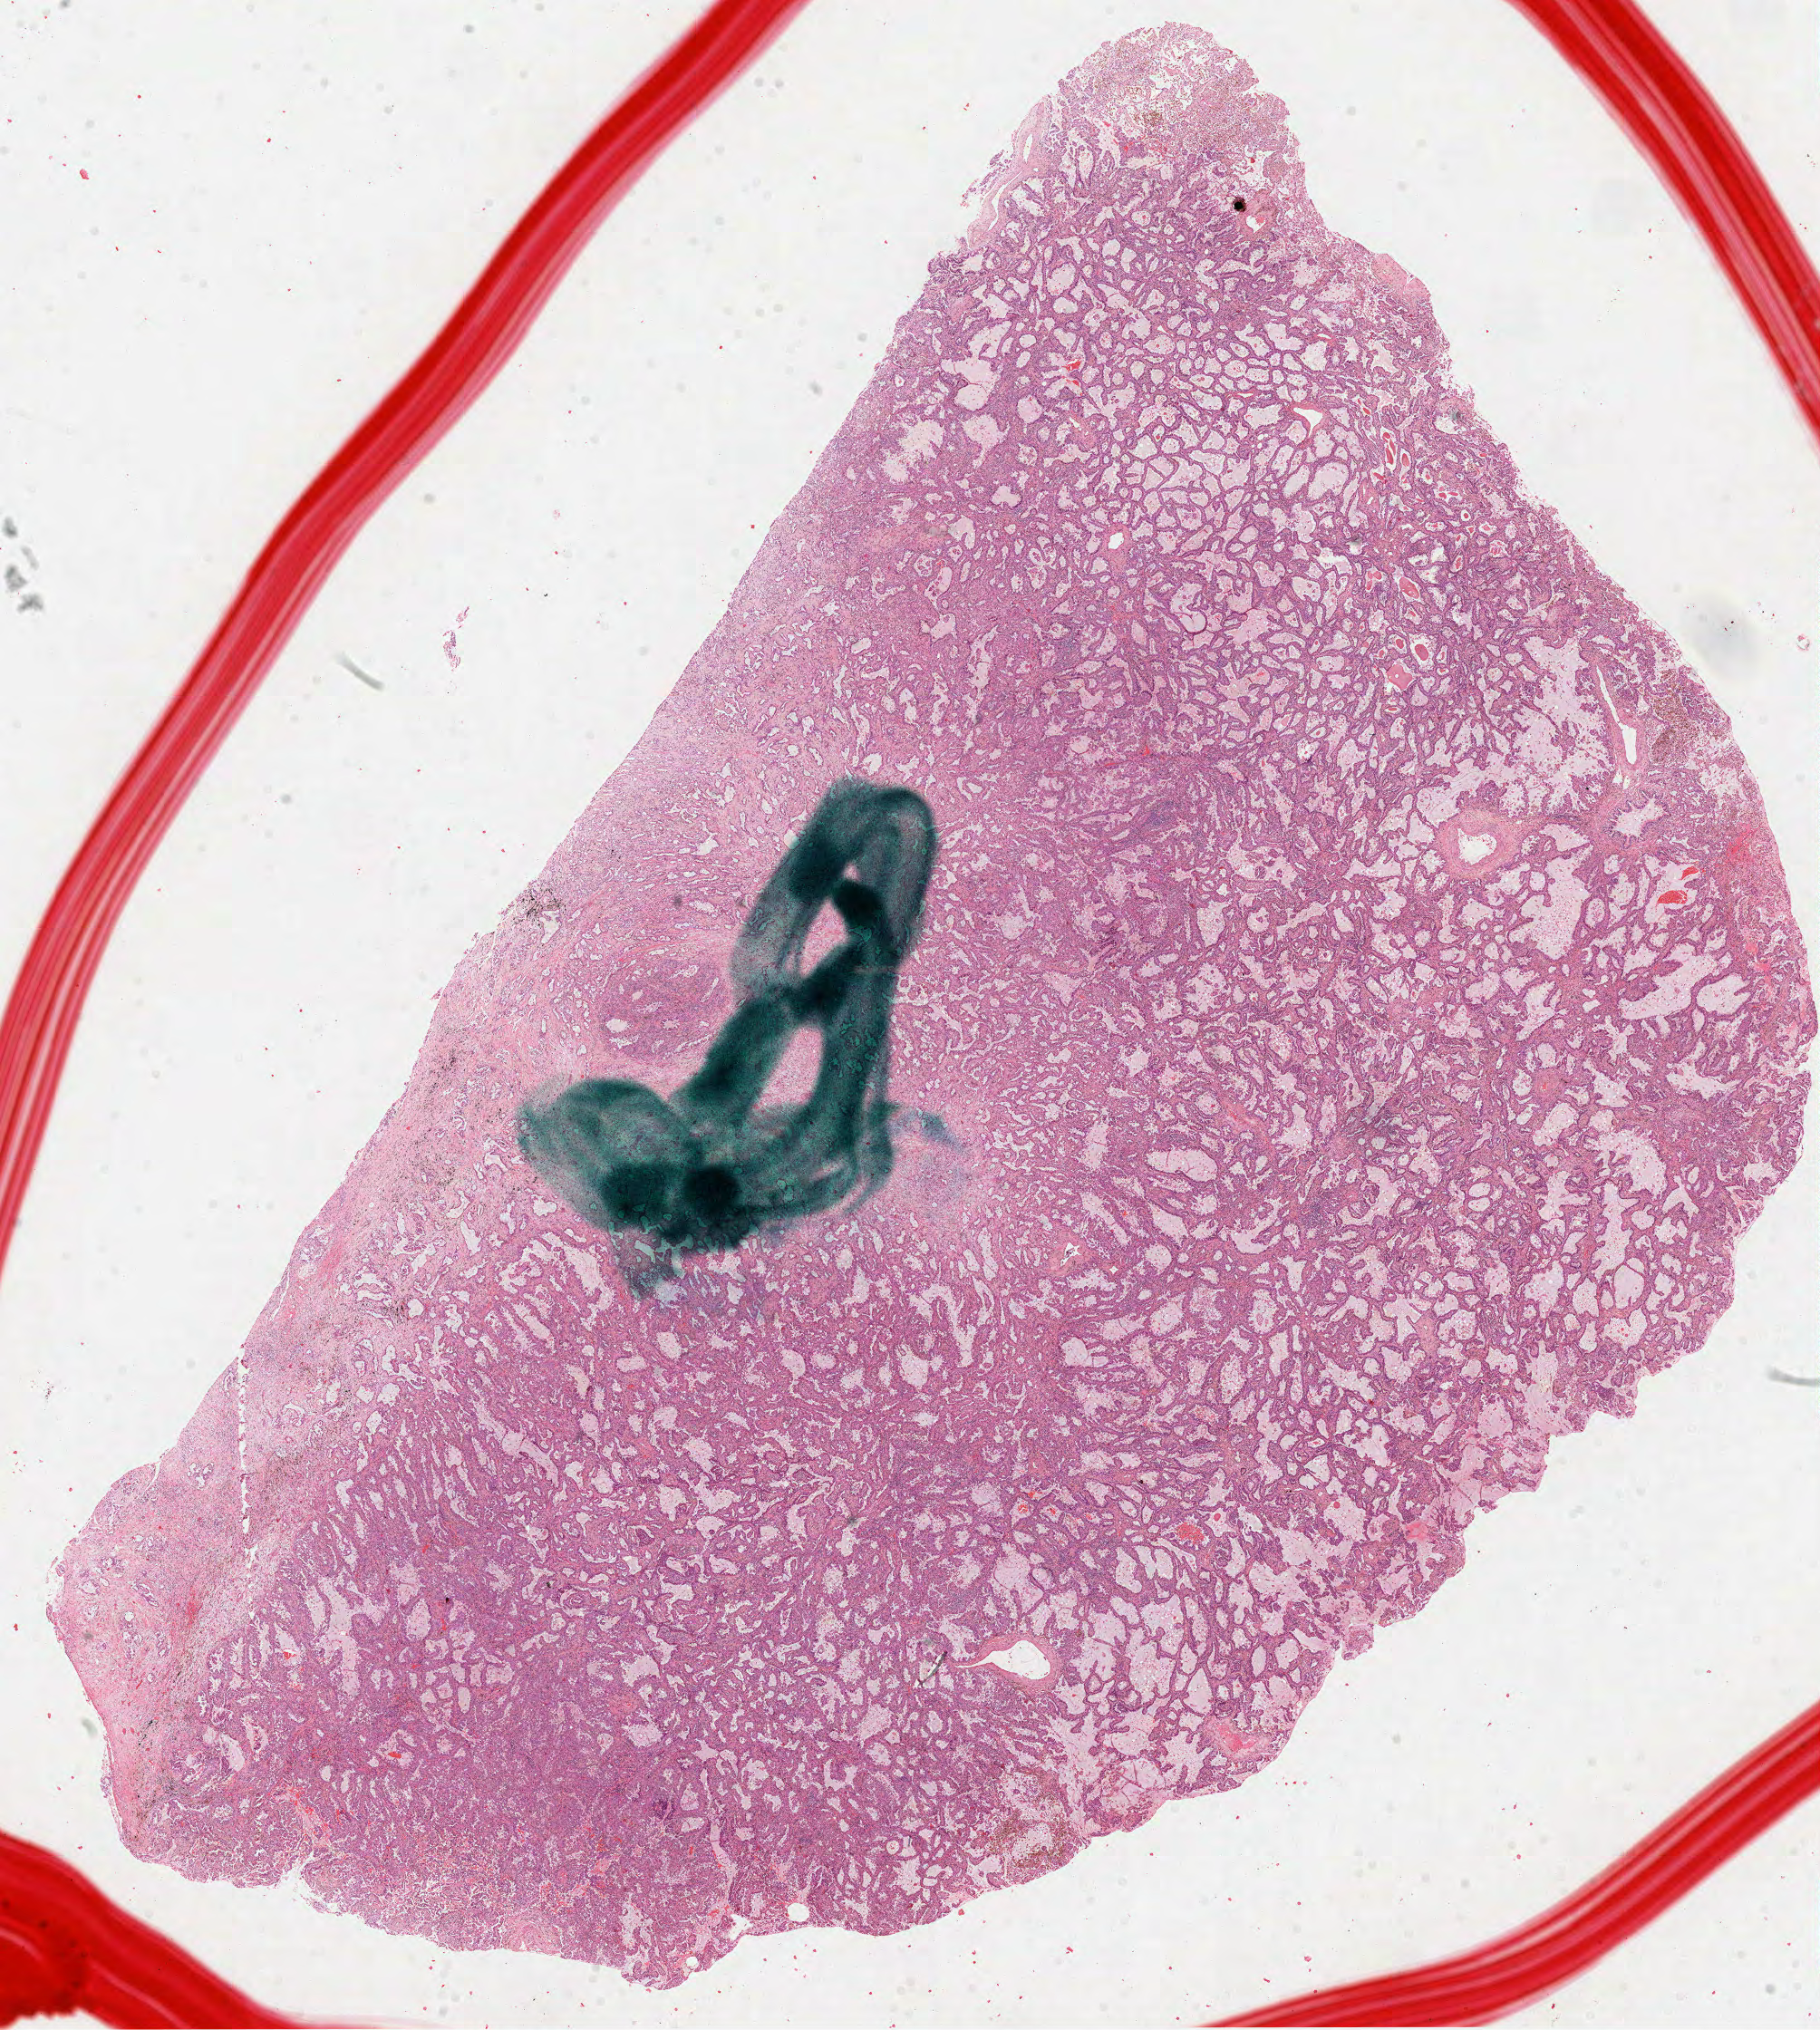
H&E whole-slide image — shown as a low-resolution overview of the whole scanned area (about 16.2 x 18.1 mm, from a 40x scan); FFPE section; primary tumour sample from the lung. Patient: female, age at initial diagnosis 61 years.
Pathologic diagnosis: Adenocarcinoma with mixed subtypes (lower lobe, lung).